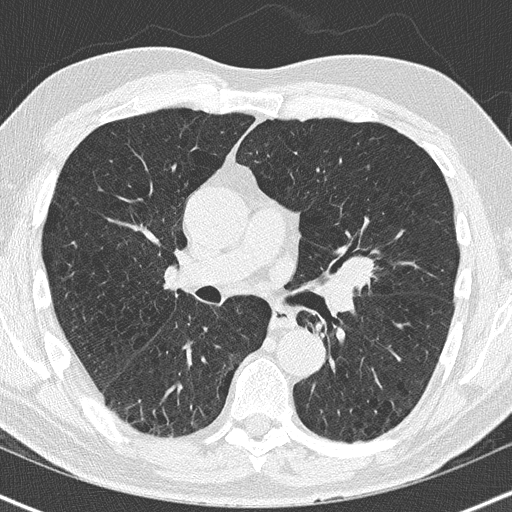
Low-dose screening chest CT, one axial slice. Position 89 of 163 along the scan axis. 120 kVp. Lung window (W 1500 / L -600 HU). 2 mm slice thickness. 512 × 512 image matrix, field of view 320 × 320 mm.
Annotated regions visible in this slice (manually delineated by an expert):
- lesion 1 (tumor, upper lobe of left lung): box from (x=337, y=255) to (x=376, y=291) px